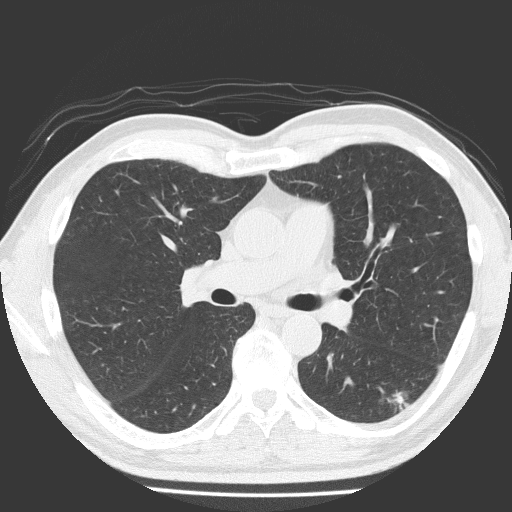
Axial slice from a low-dose chest CT screening exam; first (baseline) screen; lung window (W 1500 / L -600 HU); 2 mm slice thickness; 512 × 512 image matrix, field of view 348 × 348 mm. Male participant, aged 58 years at enrolment. Current smoker at enrolment.
• Expert-annotated lung lesion, bounding box [x1, y1, x2, y2] px = [366, 374, 426, 423].
• The screening reader recorded 4 non-calcified nodules or masses ≥4 mm on this exam; which of them this box marks is not recorded.
• Participant outcome: lung cancer diagnosed 99 days after this screen — adenosquamous carcinoma, left lower lobe, moderately differentiated (G2), stage IA (AJCC 6th edition), 28 mm at pathology.